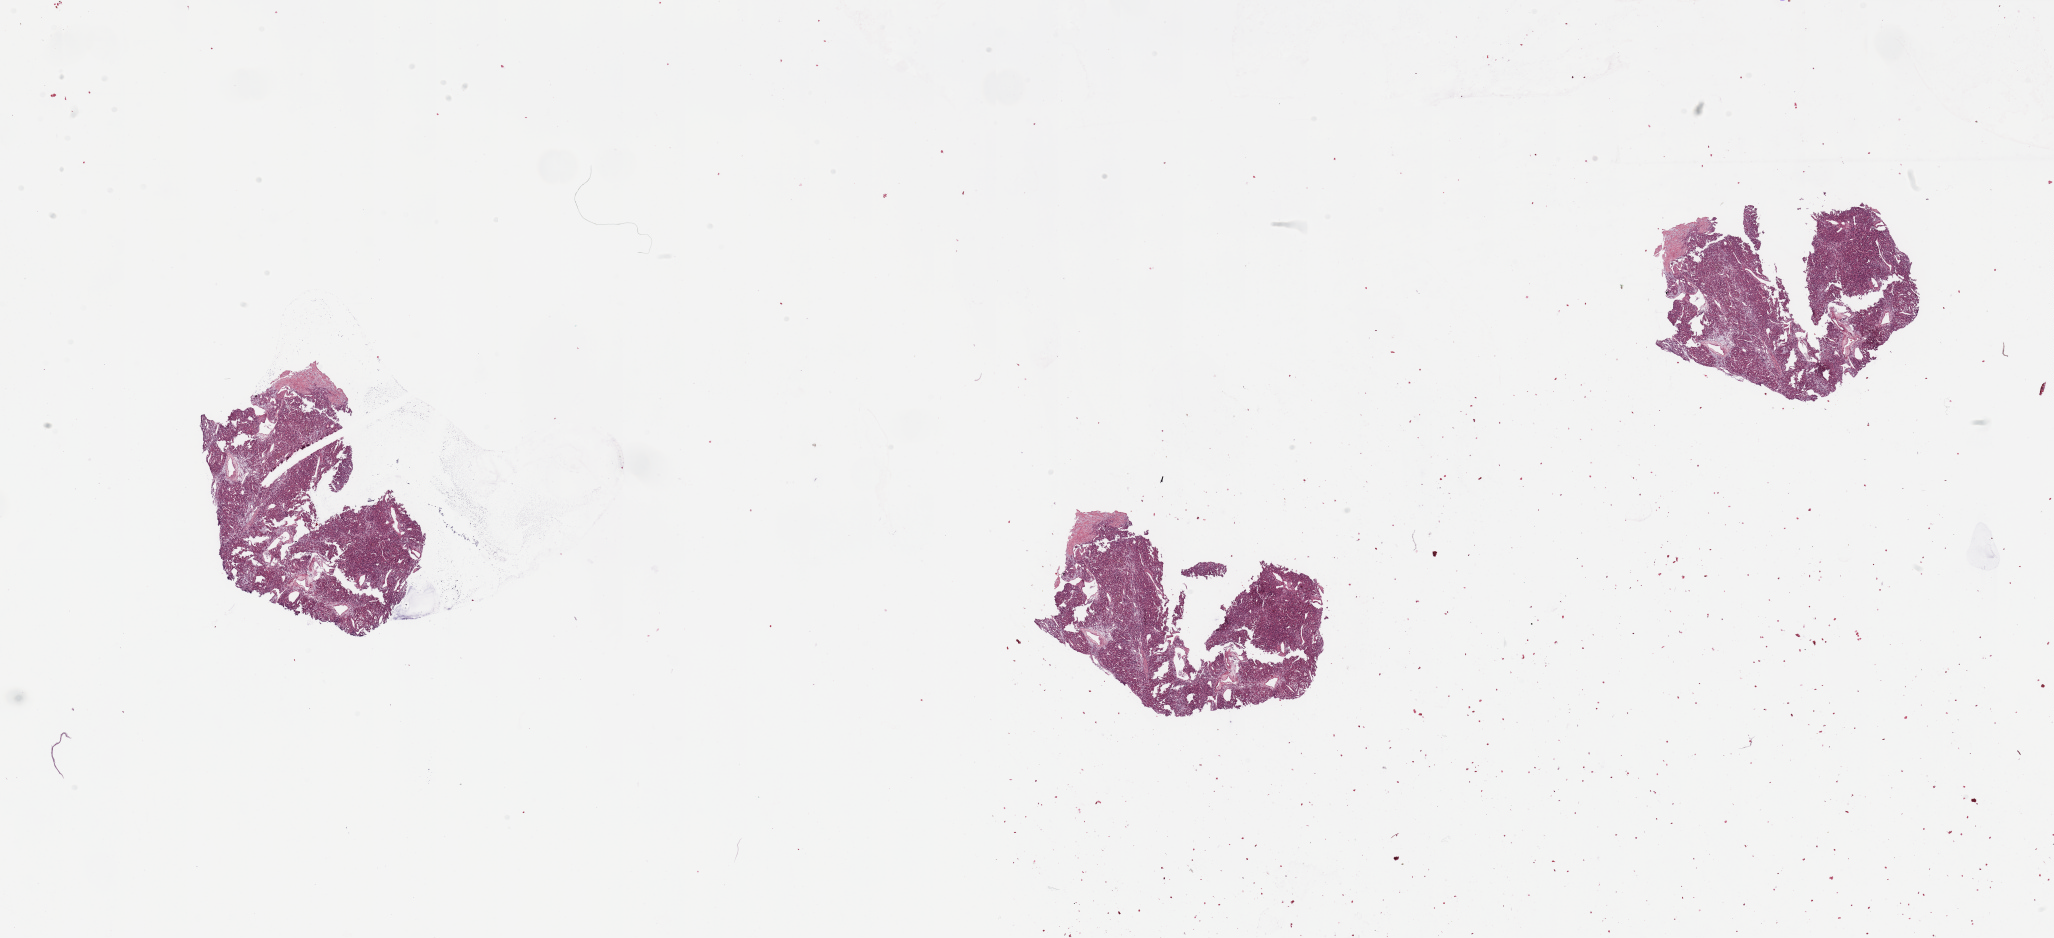
H&E-stained whole-slide image, whole scanned area (about 32.5 x 14.8 mm, from a 20x scan) shown as a low-resolution overview; tumour tissue sample, sampled site: kidney. Male, 51 y/o.
Diagnosis: Renal cell carcinoma, NOS.